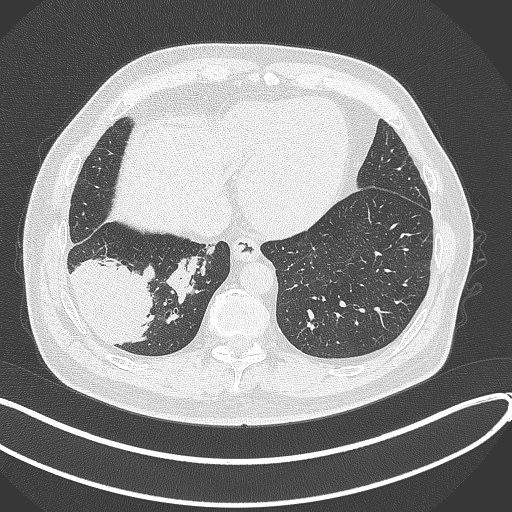
Chest CT, one axial slice. Slice 87 of 360 in the series (ordered by position). Reconstruction kernel B70f. Lung window (W 1500 / L -600 HU). 1 mm slice thickness. 512 × 512 image matrix, field of view 400 × 400 mm. Male patient, age 59 years.
Annotated regions visible in this slice (rectangle marked by the reading radiologist):
- lung tumour (recorded histology: adenocarcinoma): bounding box [x1, y1, x2, y2] px = [72, 254, 155, 348]